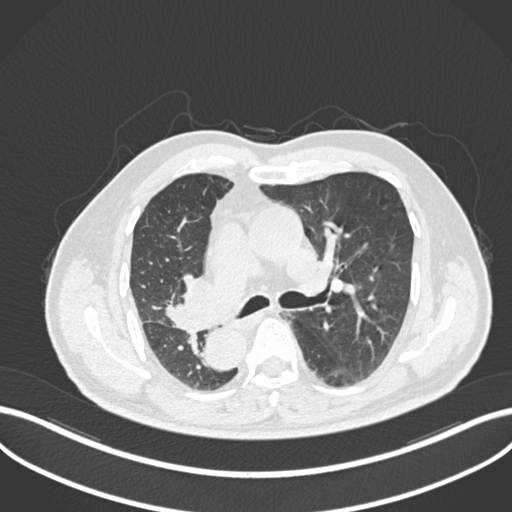
Chest CT, one axial slice; slice 139 of 206 in the series (ordered by position); 120 kVp; lung window (W 1500 / L -600 HU); 512 × 512 image matrix, field of view 400 × 400 mm. Patient: male, 67 years. From the clinical record (not read from this slice): clinical TNM (as recorded): T2a N0 M0.
Outlined on this slice (rectangle marked by the reading radiologist):
- lung tumour (recorded histology: squamous cell carcinoma): bounding box <162,269,226,335> (left, top, right, bottom; pixels)